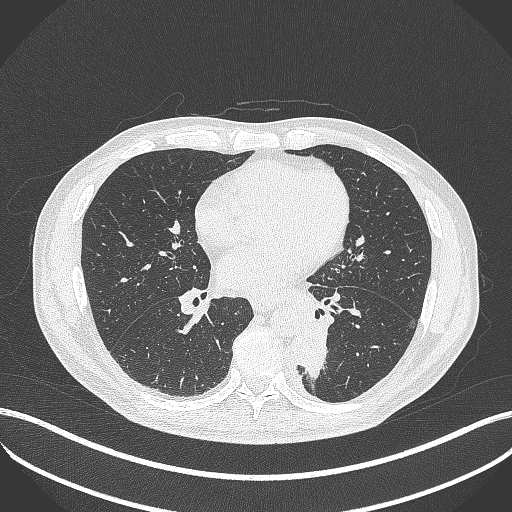
Chest CT, one axial slice. Reconstruction kernel B70f. 120 kVp. Lung window (W 1500 / L -600 HU). 1 mm slice thickness. 512 × 512 image matrix. Male patient, age 72 years. Case-level facts recorded for this patient, not image findings: clinical TNM (as recorded): T2b N0 M1.
Outlined on this slice (bounding box drawn by a radiologist):
- lung tumour (recorded histology: adenocarcinoma): box from (x=294, y=314) to (x=333, y=383) px